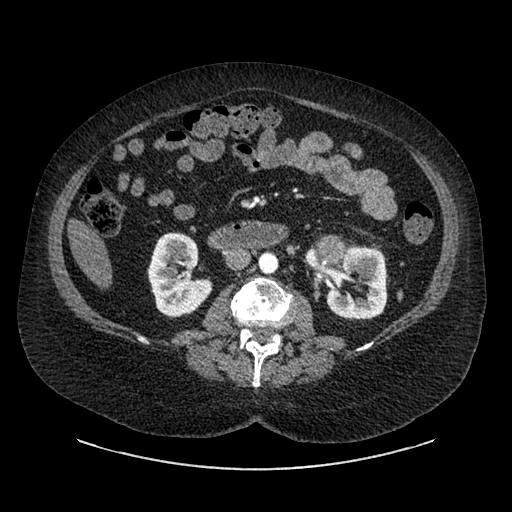
Contrast-enhanced abdominal CT, one axial slice; position 485 of 769 along the scan axis; 120 kVp; intravenous contrast given; soft-tissue window (W 400 / L 40 HU); 0.62 mm slice thickness; 512 × 512 image matrix, field of view 460 × 460 mm. Patient: female, 61 years. From the clinical record (not read from this slice): diagnosis: adrenocortical carcinoma; tumour side: left adrenal; tumour size at pathology: 13 cm; Ki-67 index: 79 %; stage (as recorded): 2.
Structures marked on this image (semi-automatic segmentation, software-assisted and operator-edited):
- mass: bounding box <326,246,339,262> (left, top, right, bottom; pixels)